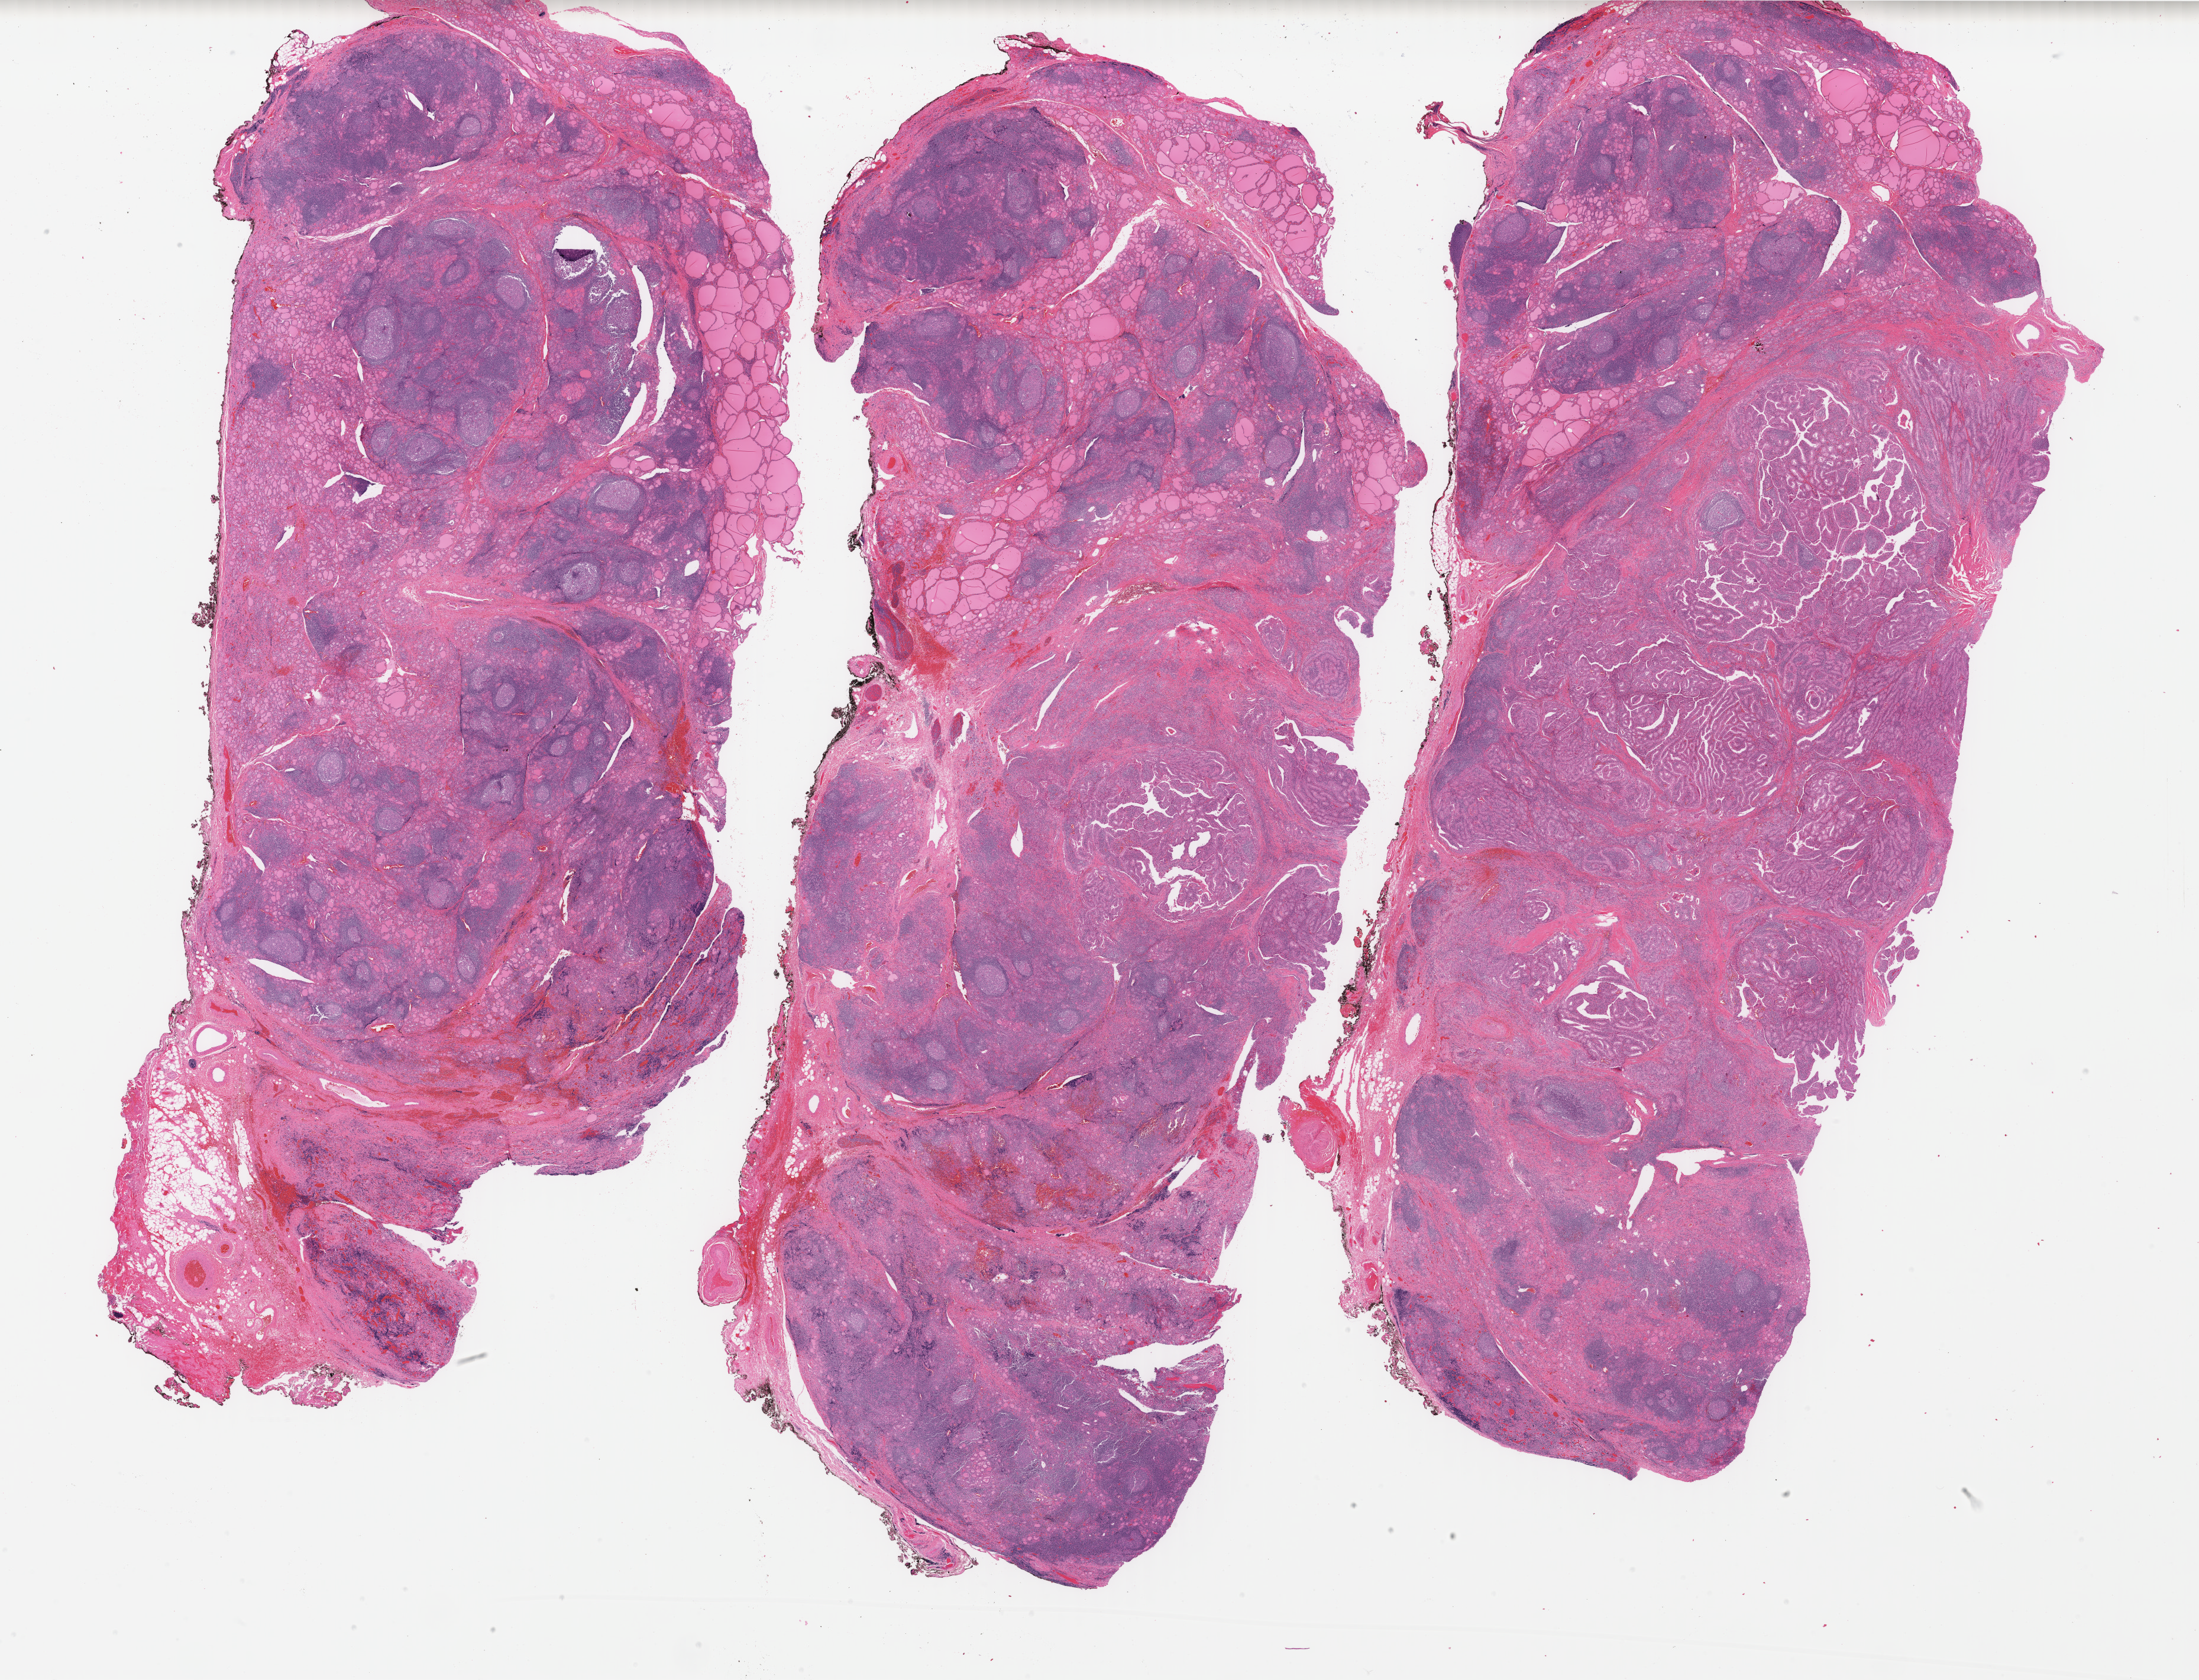
Digitized H&E tissue section (whole slide), low-resolution overview of the scanned area, about 29.5 x 22.6 mm, FFPE section, thyroid, primary tumour sample. Patient: female, age at initial diagnosis 21 years.
Histologic diagnosis: Papillary adenocarcinoma, NOS (thyroid gland). Lymph nodes positive (case pathology): 1 of 2 examined. Laterality: left. AJCC pathologic stage: I (6th edition).